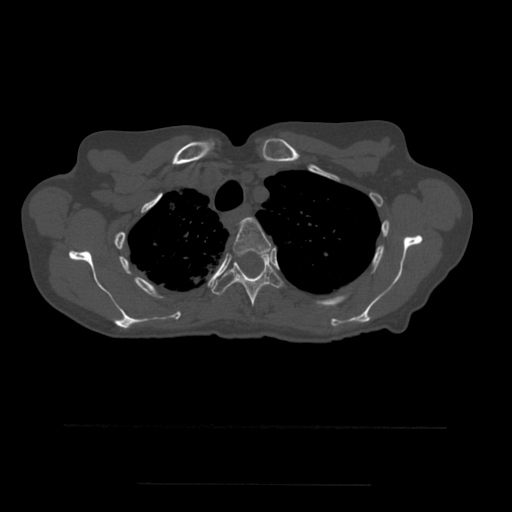
CT including the spine, one axial slice; position 413 of 544 along the scan axis; bone window (W 1800 / L 400 HU); 1.25 mm slice thickness; 512 × 512 image matrix, field of view 350 × 350 mm. Patient age 58 years. Case-level facts recorded for this patient, not image findings: primary cancer: lung.
Structures marked on this image (semi-automatically segmented with operator editing):
- T3 vertebra: box from (x=233, y=218) to (x=272, y=255) px
- T4 vertebra: (x=212, y=252)–(x=286, y=306)